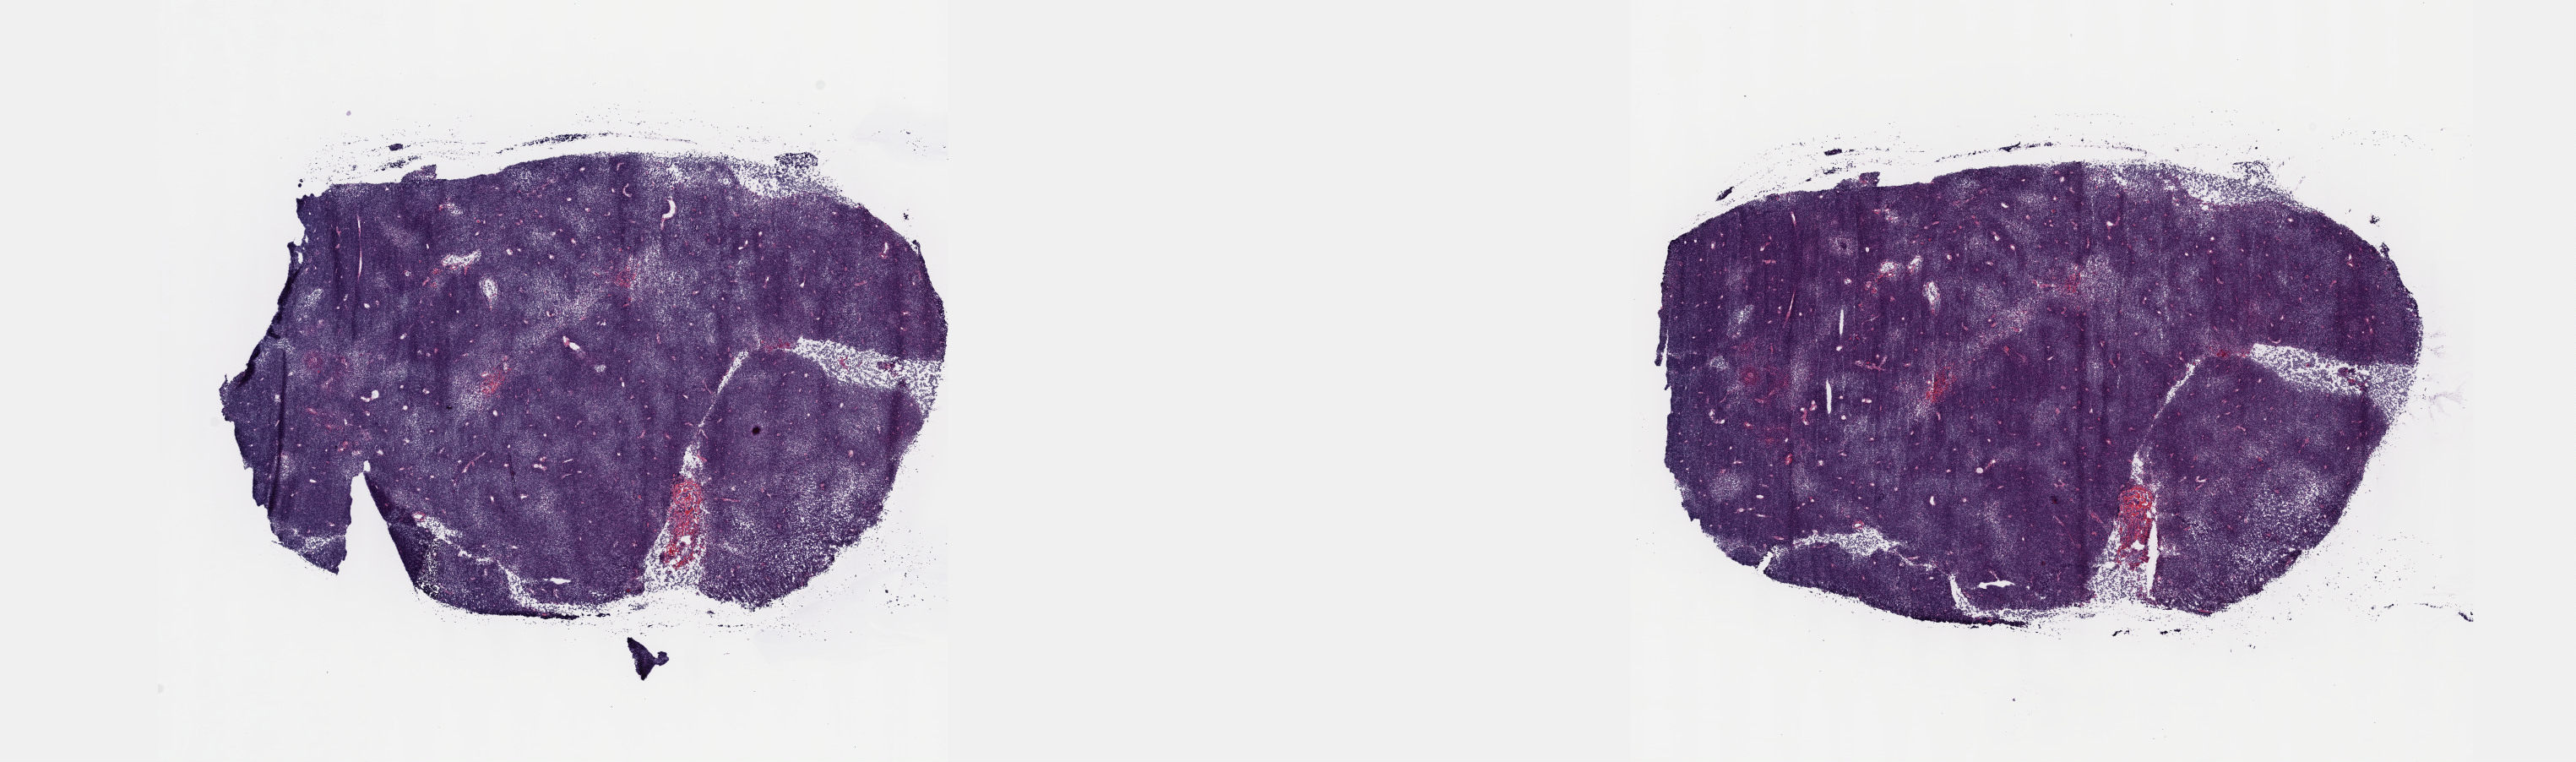
Digitized H&E tissue section (whole slide) — whole scanned area (about 24.6 x 7.3 mm, acquisition: 40x scan) shown as a low-resolution overview. Frozen section from the top of the tissue portion. Thymus, primary tumour sample. Female patient; age at initial diagnosis 46 years. Composition of this section per pathologist review: tumour cells 95%, tumour nuclei 95%, normal cells 0%, stromal cells 5%, necrosis 0%. Infiltration values recorded for this section: lymphocyte infiltration 0%, monocyte infiltration 0%, neutrophil infiltration 0%.
Histologic diagnosis: Thymoma, type B1, malignant.